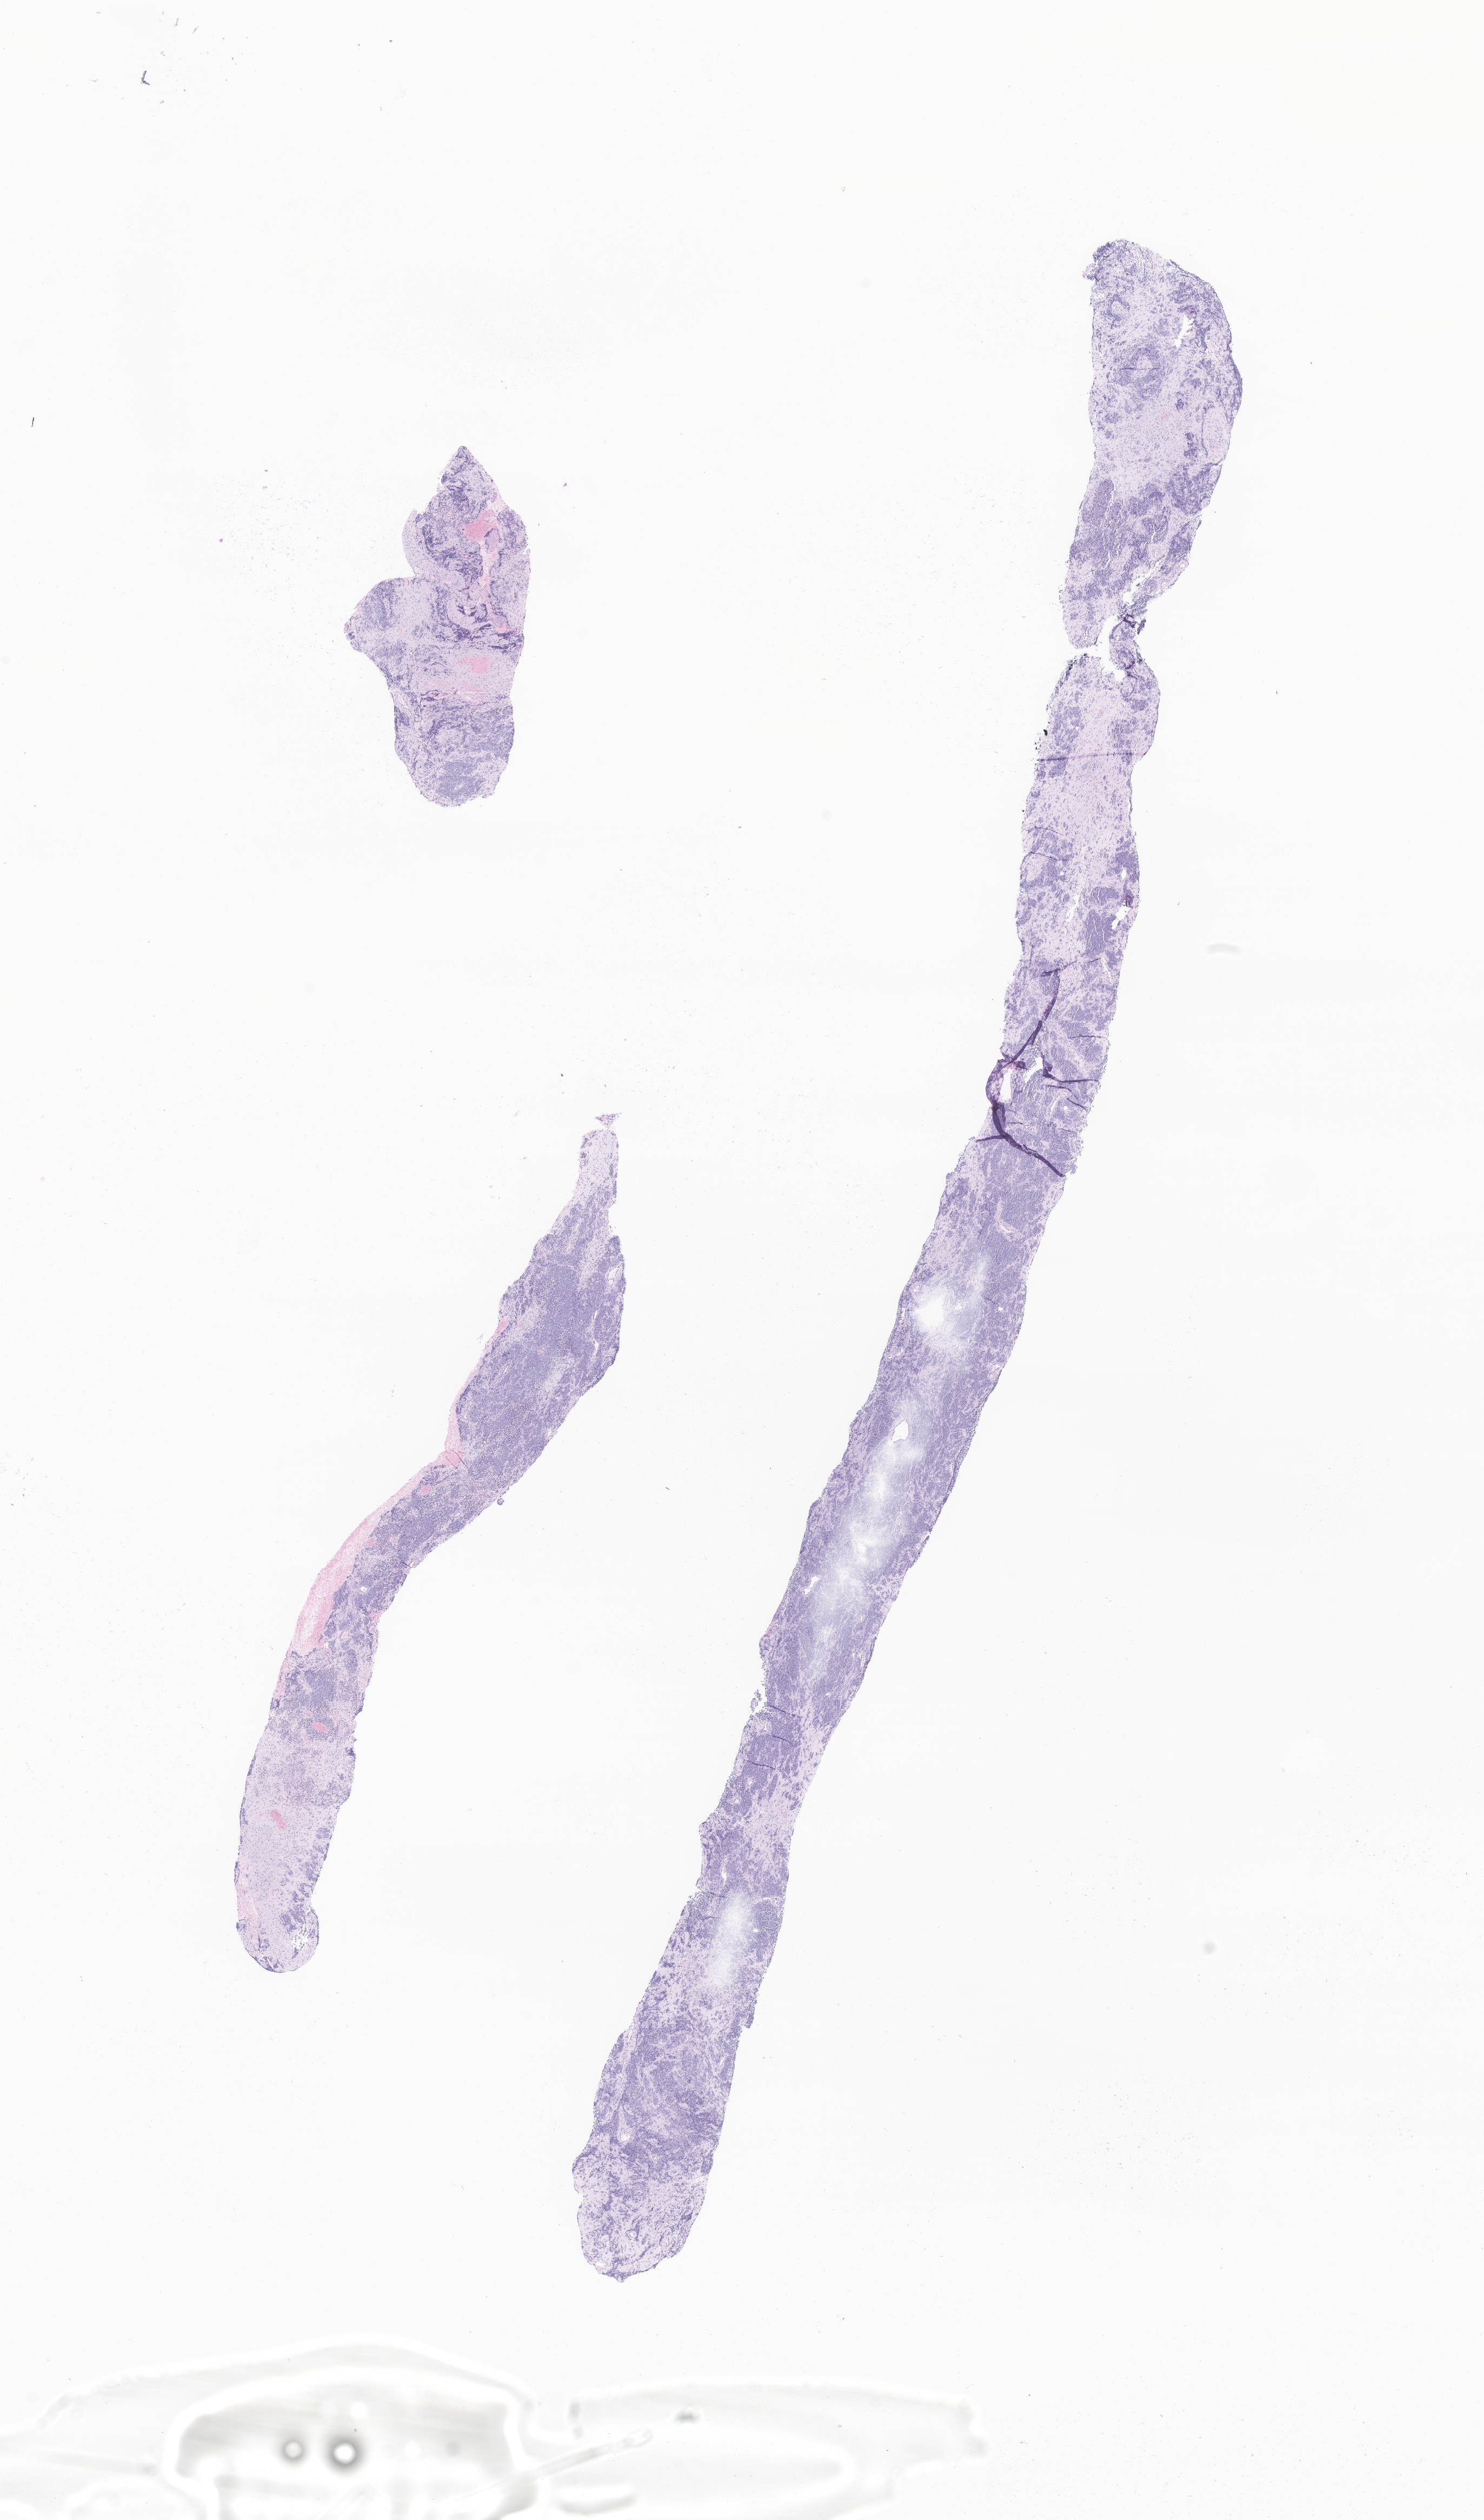
Digitized H&E-stained section of tumor tissue from the pancreas, low-resolution overview of the scanned area, about 11.6 x 19.7 mm; formalin-fixed, paraffin-embedded (FFPE) tissue. Patient: male, age 184 months (15 years 4 months).
* diagnosis: Sarcoma, NOS